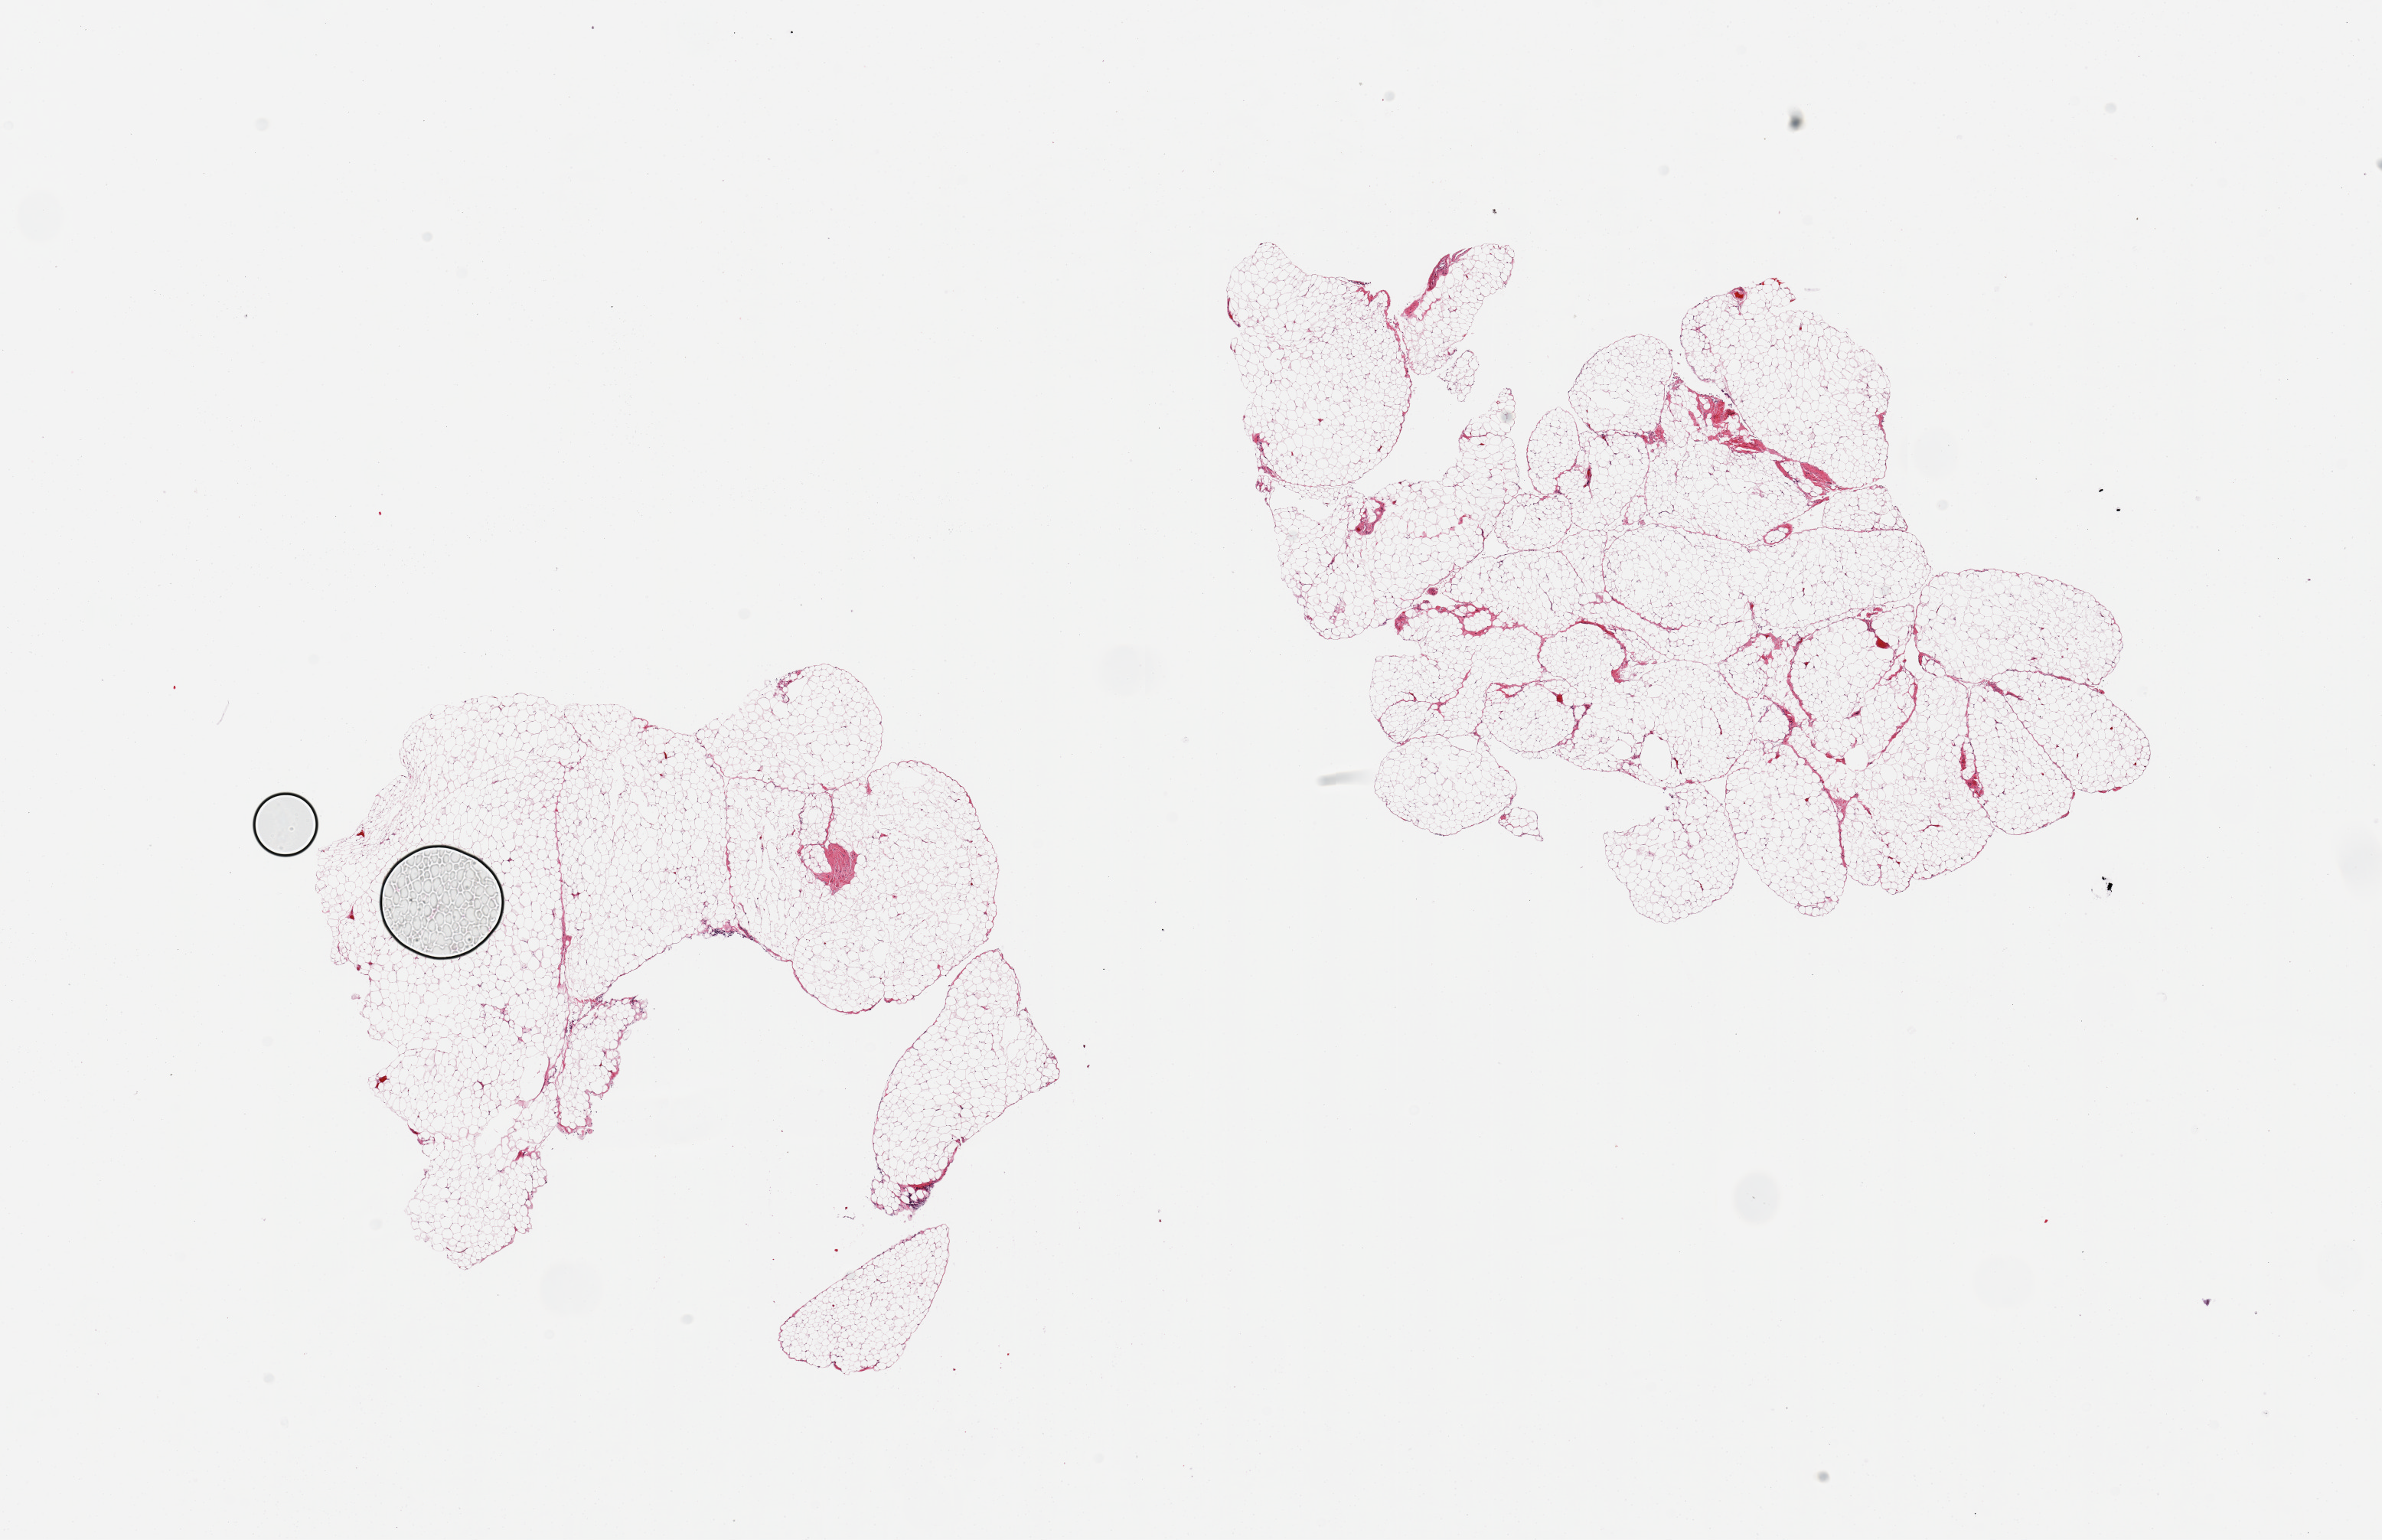
Whole-slide image, H&E stain — a low-resolution overview of the entire scanned area, about 24.6 x 15.9 mm (from a 20x scan); PAXgene-fixed, paraffin-embedded tissue; section of omentum (target tissue); donor tissue sample.
Pathologist's review note for this sample: 2 pieces.